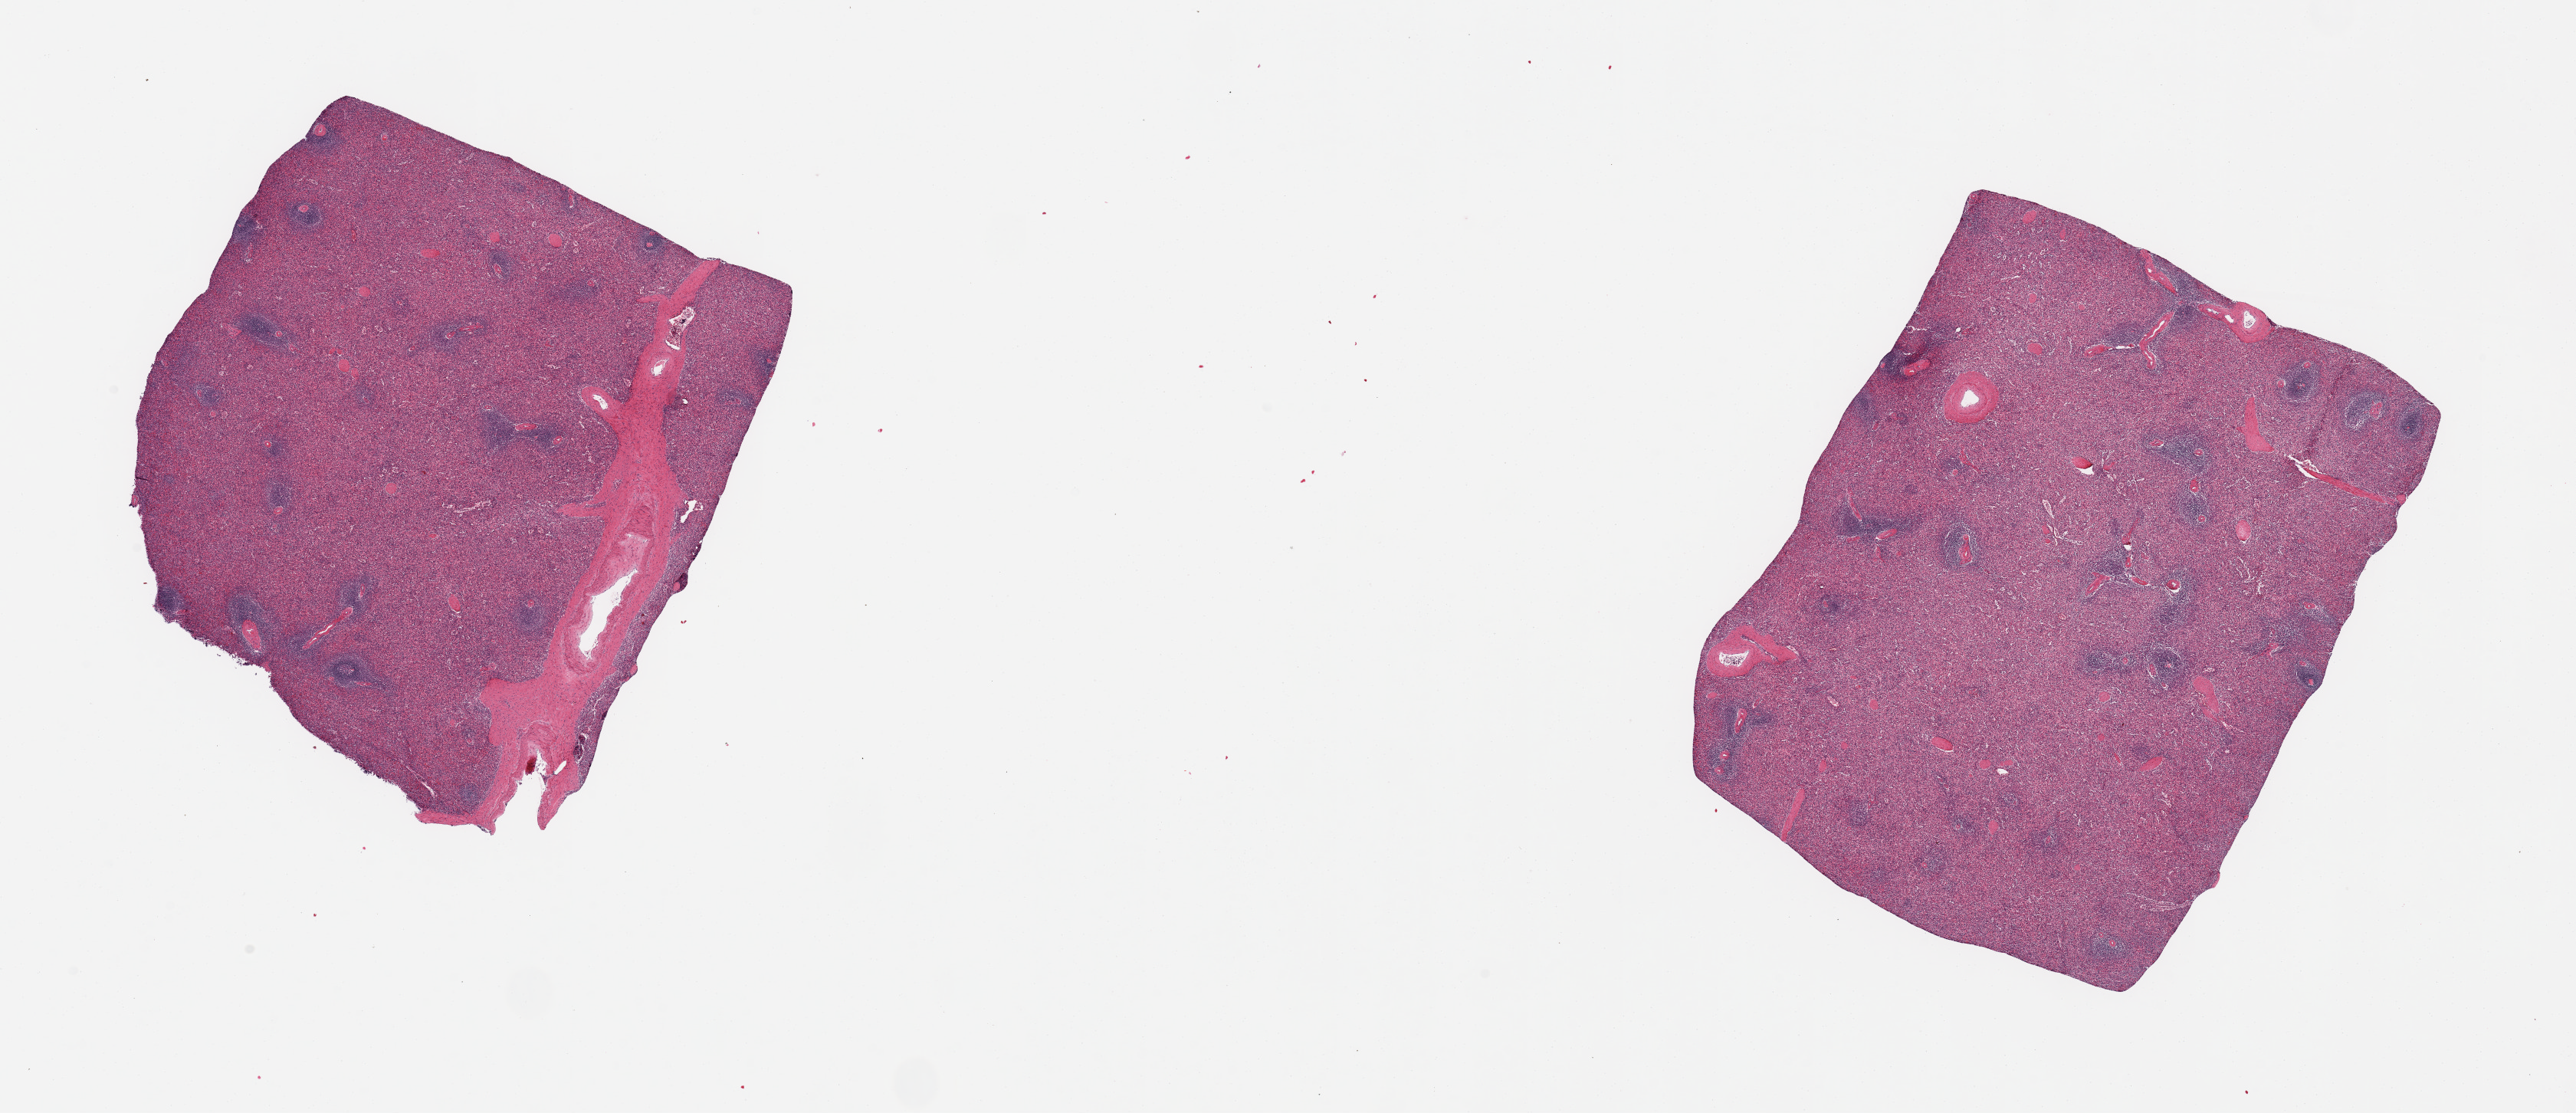
Haematoxylin and eosin whole-slide image — low-resolution overview of the scanned area, about 26.6 x 11.5 mm (acquisition: 20x scan). PAXgene-fixed paraffin-embedded (PFPE) section. Target tissue: spleen. Donor tissue sample. Donor: male.
Pathologist's review note for this sample: 2 pieces; non-congested; large vessels in 1 piece [10%].